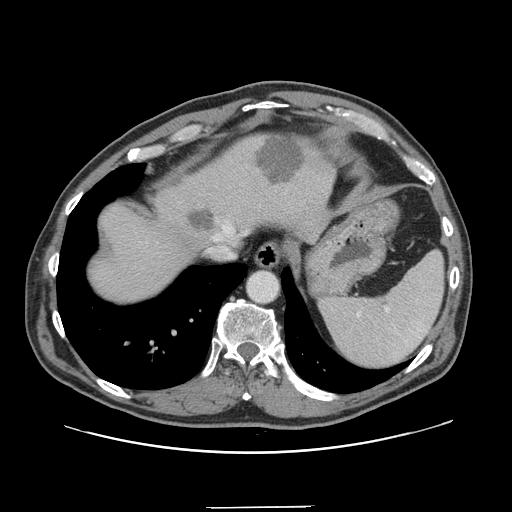
Contrast-enhanced abdominal CT, one axial slice; slice 124 of 139 in the series (ordered by position); intravenous contrast given; soft-tissue window (W 400 / L 40 HU); 512 × 512 image matrix, field of view 397 × 397 mm. Male patient, age 64 years. From the clinical record (not read from this slice): diagnosis: colorectal cancer liver metastases, imaged before liver resection; multiple liver metastases: yes; largest metastasis: 3.5 cm; disease in both lobes: yes.
Annotated regions visible in this slice (outlined manually by an expert reader):
- hepatic veins: bounding box [x1, y1, x2, y2] px = [223, 226, 226, 230]
- liver: [88, 132, 331, 304]
- planned liver remnant (the part of the liver to remain after resection): [87, 140, 257, 303]
- liver metastasis: [190, 211, 215, 231]
- liver metastasis: [256, 136, 307, 185]